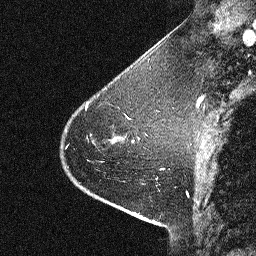
Breast MRI (dynamic contrast-enhanced), one sagittal slice; slice 15 of 64 in the series (ordered by position); dynamic contrast-enhanced study with each time point stored as its own series, time point 2 of 3 at this slice position (early post-contrast, ordered by acquisition time); 1.5 T; TE 4.5 ms, TR 11 ms; 2.06 mm slice thickness; 256 × 256 image matrix. Patient: female, 46 years. From the clinical record (not read from this slice): setting: breast cancer imaged before/during neoadjuvant chemotherapy; receptor status: HER2-positive.
Annotated regions visible in this slice (semi-automatic segmentation, software-assisted and operator-edited):
- analysis volume of interest (the breast-tissue region the enhancement analysis was run in; not a lesion): bounding box <43,80,150,180> (left, top, right, bottom; pixels)
- tumour enhancement mask (voxels above the 90 % enhancement threshold inside the analysis volume of interest): <113,117,127,138>